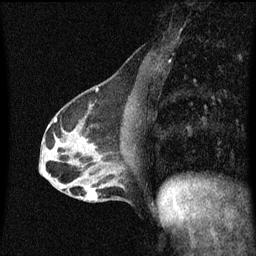
Breast MRI (dynamic contrast-enhanced), one sagittal slice. Position 24 of 60 along the scan axis. Dynamic contrast-enhanced series, image 2 of 3 at this slice position (ordered by acquisition). 1.5 T. TE 4.2 ms, TR 8.4 ms. 2 mm slice thickness. 256 × 256 image matrix. Female patient, age 40 years.
Outlined on this slice (semi-automatic segmentation, software-assisted and operator-edited):
- analysis volume of interest (the breast-tissue region the enhancement analysis was run in; not a lesion): box from (x=78, y=166) to (x=120, y=203) px
- tumour enhancement mask (voxels above the 70 % enhancement threshold inside the analysis volume of interest): (x=82, y=190)–(x=98, y=201)